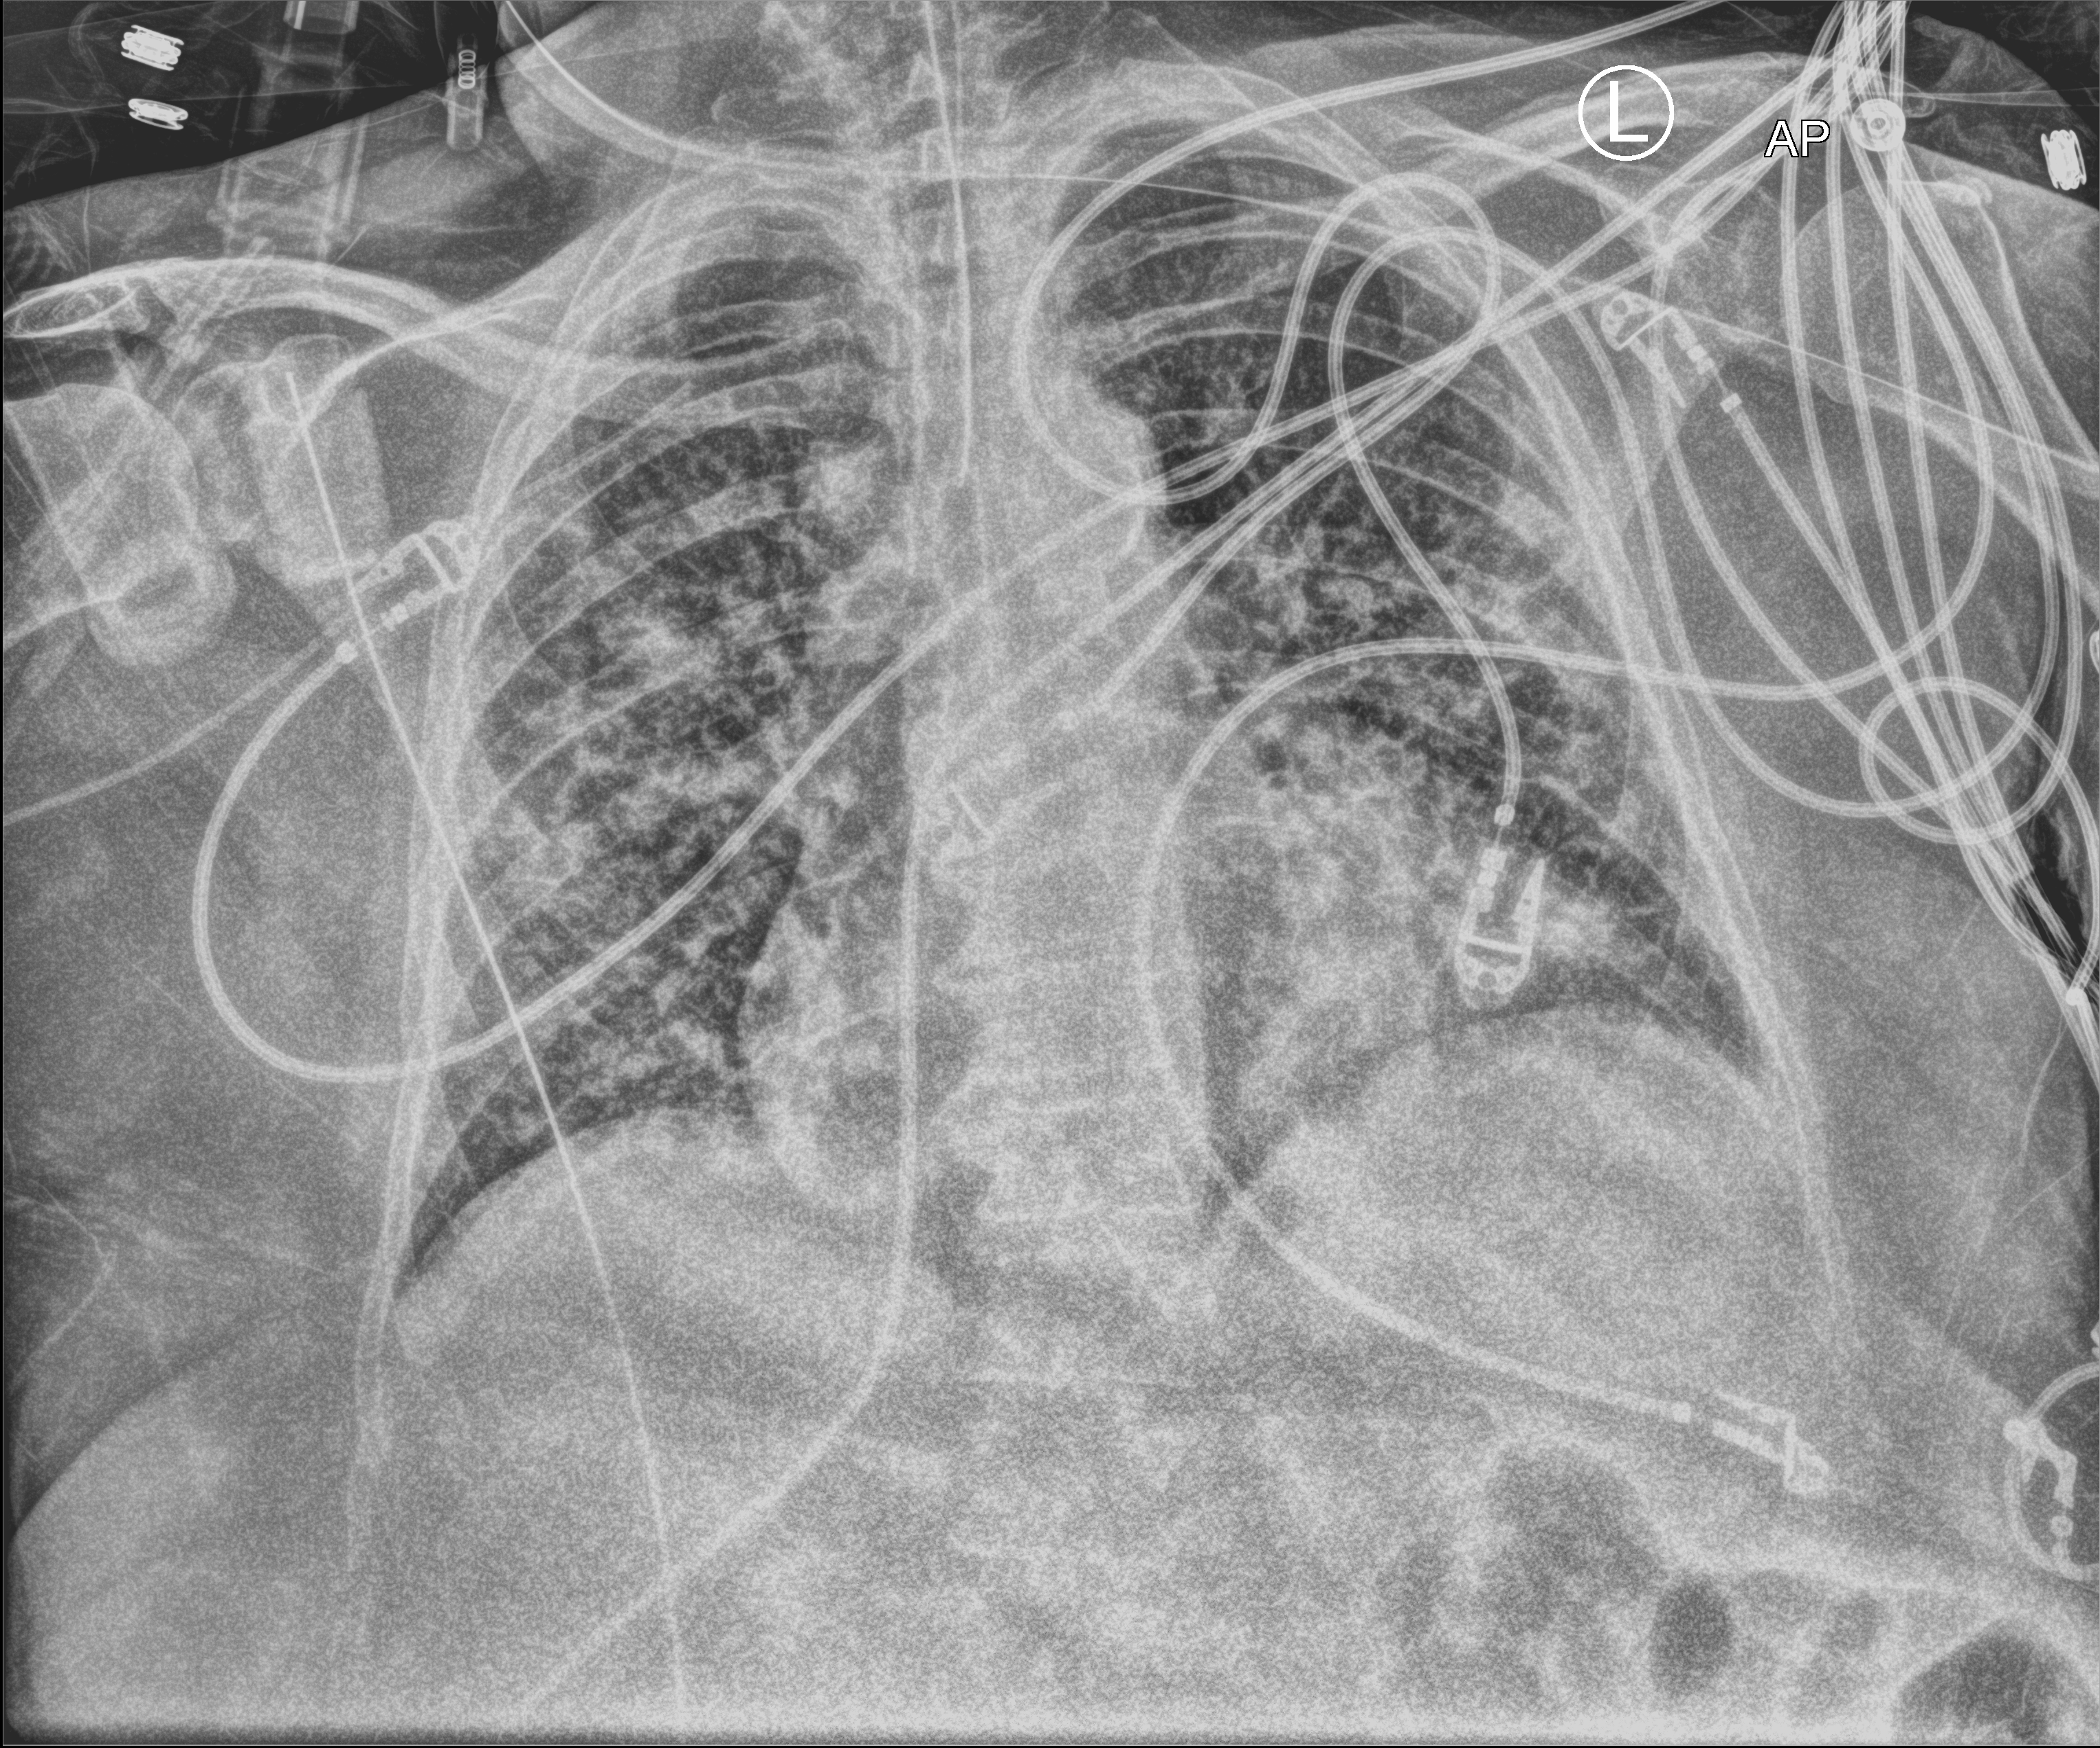
Bedside chest radiograph (computed radiography); anteroposterior (AP) projection. Patient hospitalised with COVID-19; female, aged 75–90 years.
Admission-level facts for this patient (not findings on this image; timing relative to this image not recorded): admitted to intensive care during this hospital stay: yes; COPD (admission record): yes; mechanically ventilated during this hospital stay: yes.